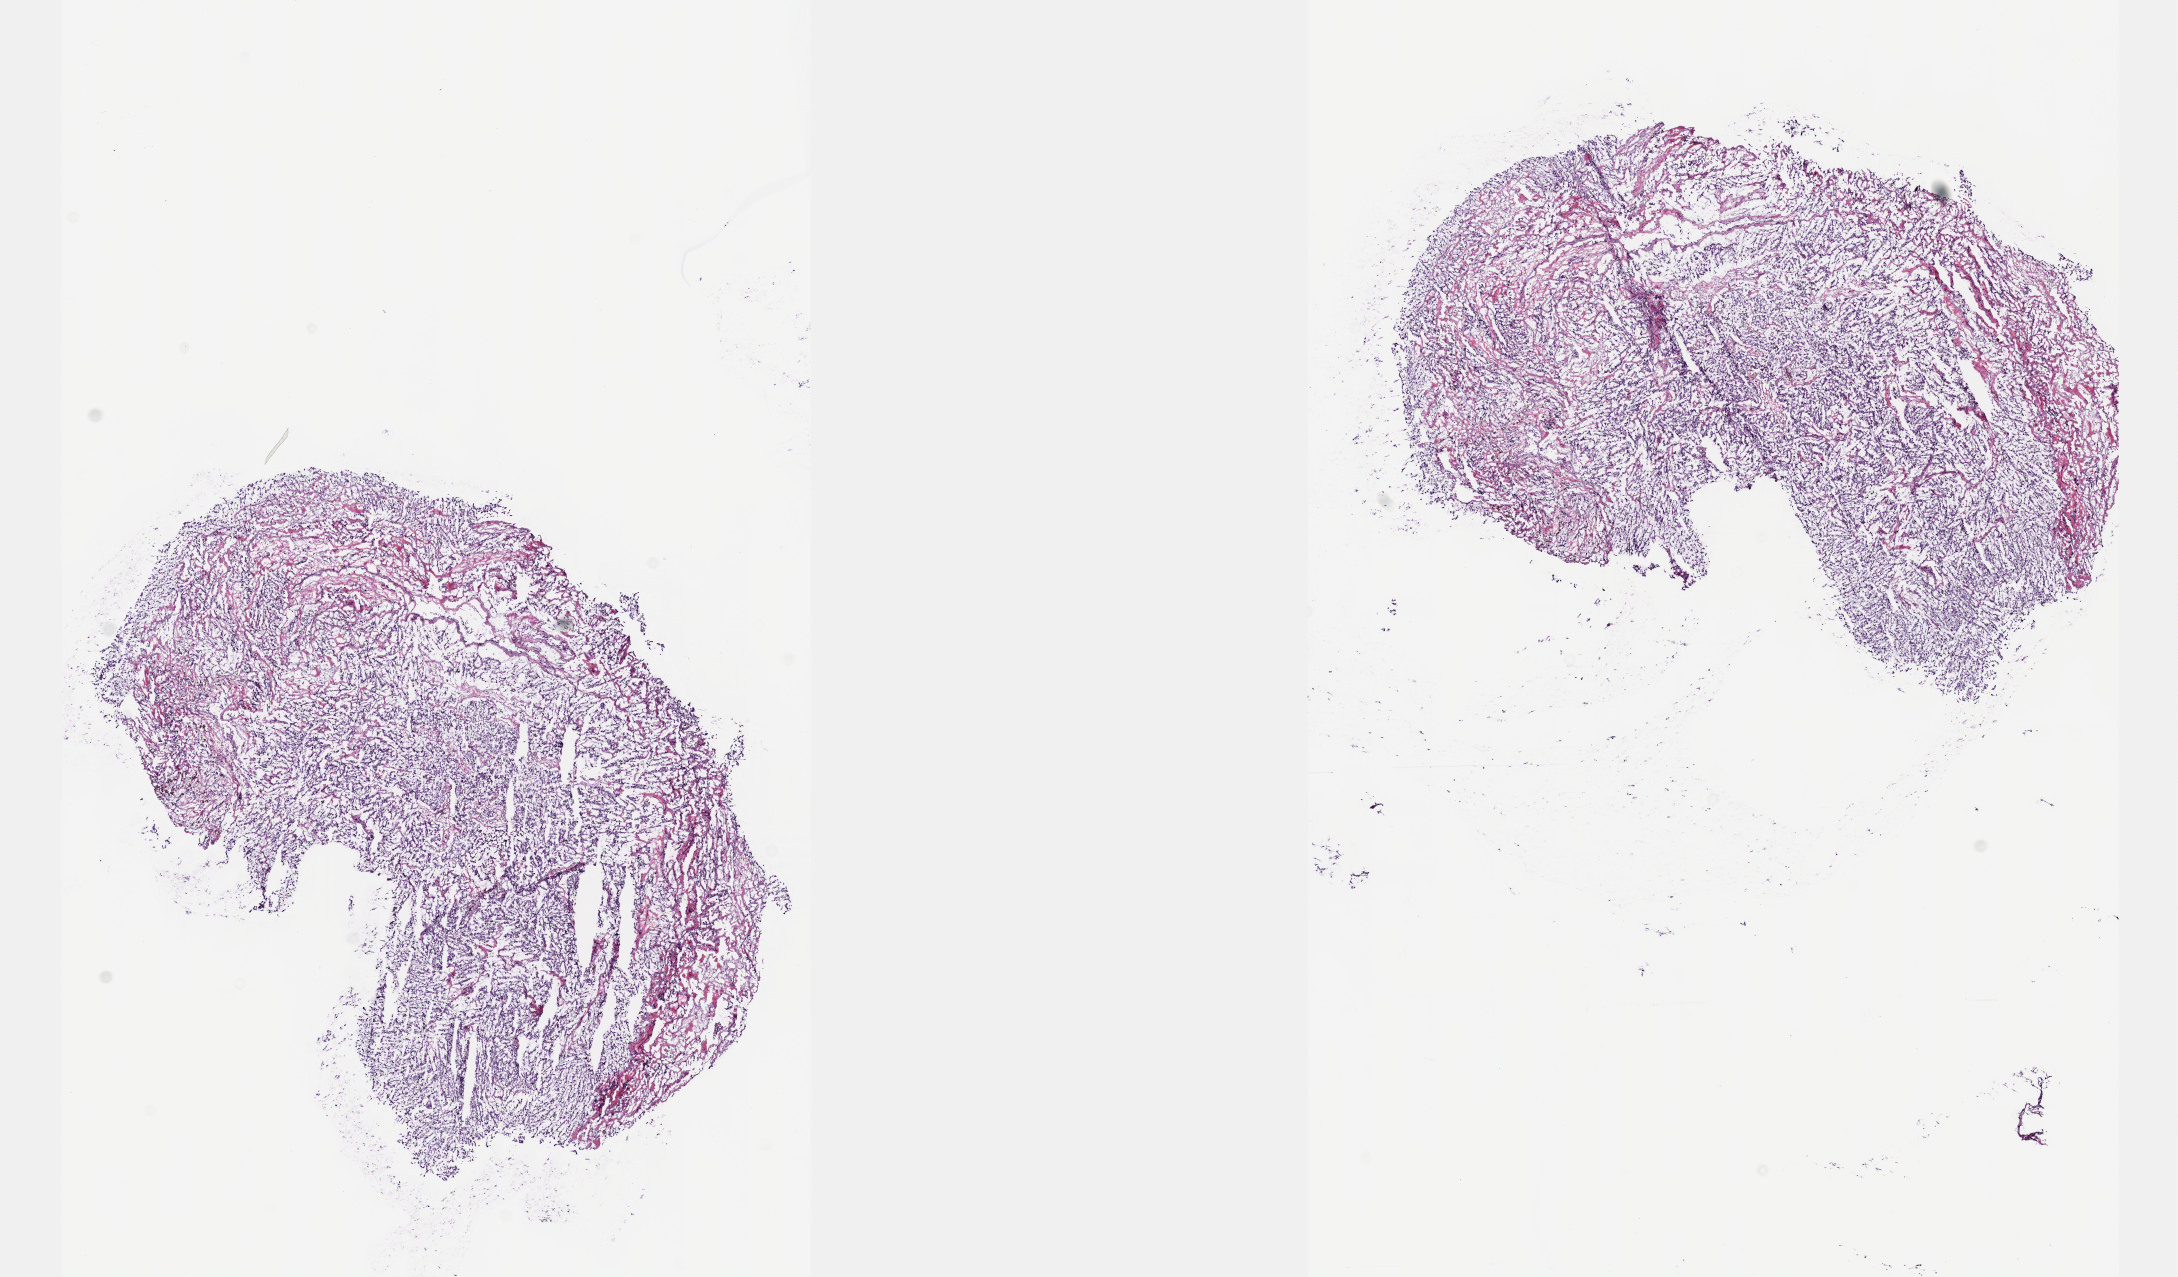
H&E whole-slide image — whole scanned area (about 17.6 x 10.3 mm, acquisition: 40x scan) shown as a low-resolution overview. Frozen section. Sample: primary tumour, adrenal gland. Male patient; age at initial diagnosis 40 years. Pathologist review of this section (percent, as recorded): tumour cells 75%, tumour nuclei 75%, normal cells 0%, stromal cells 25%, necrosis 0%. Inflammatory infiltration, as recorded: lymphocyte infiltration 0%, monocyte infiltration 0%, neutrophil infiltration 0%.
Laterality: left. Diagnosis: Pheochromocytoma, NOS.